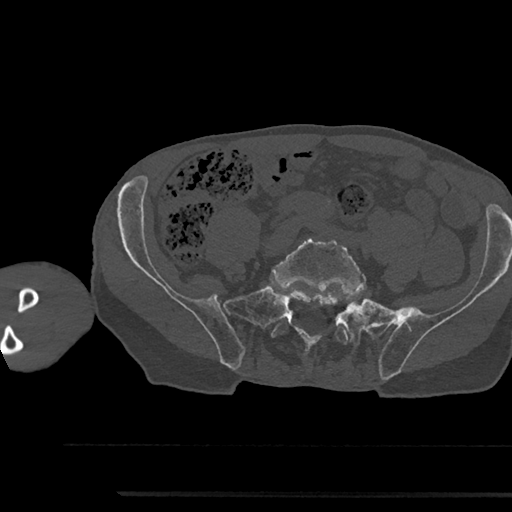
CT including the spine, one axial slice; position 317 of 797 along the scan axis; reconstruction kernel Br40s/3; 120 kVp; bone window (W 1800 / L 400 HU); 0.5 mm slice thickness; 512 × 512 image matrix, field of view 367 × 367 mm. Male patient, age 79 years. Case-level facts recorded for this patient, not image findings: primary cancer: prostate.
Annotated regions visible in this slice (semi-automatically segmented with operator editing):
- L5 vertebra: box from (x=270, y=235) to (x=366, y=344) px